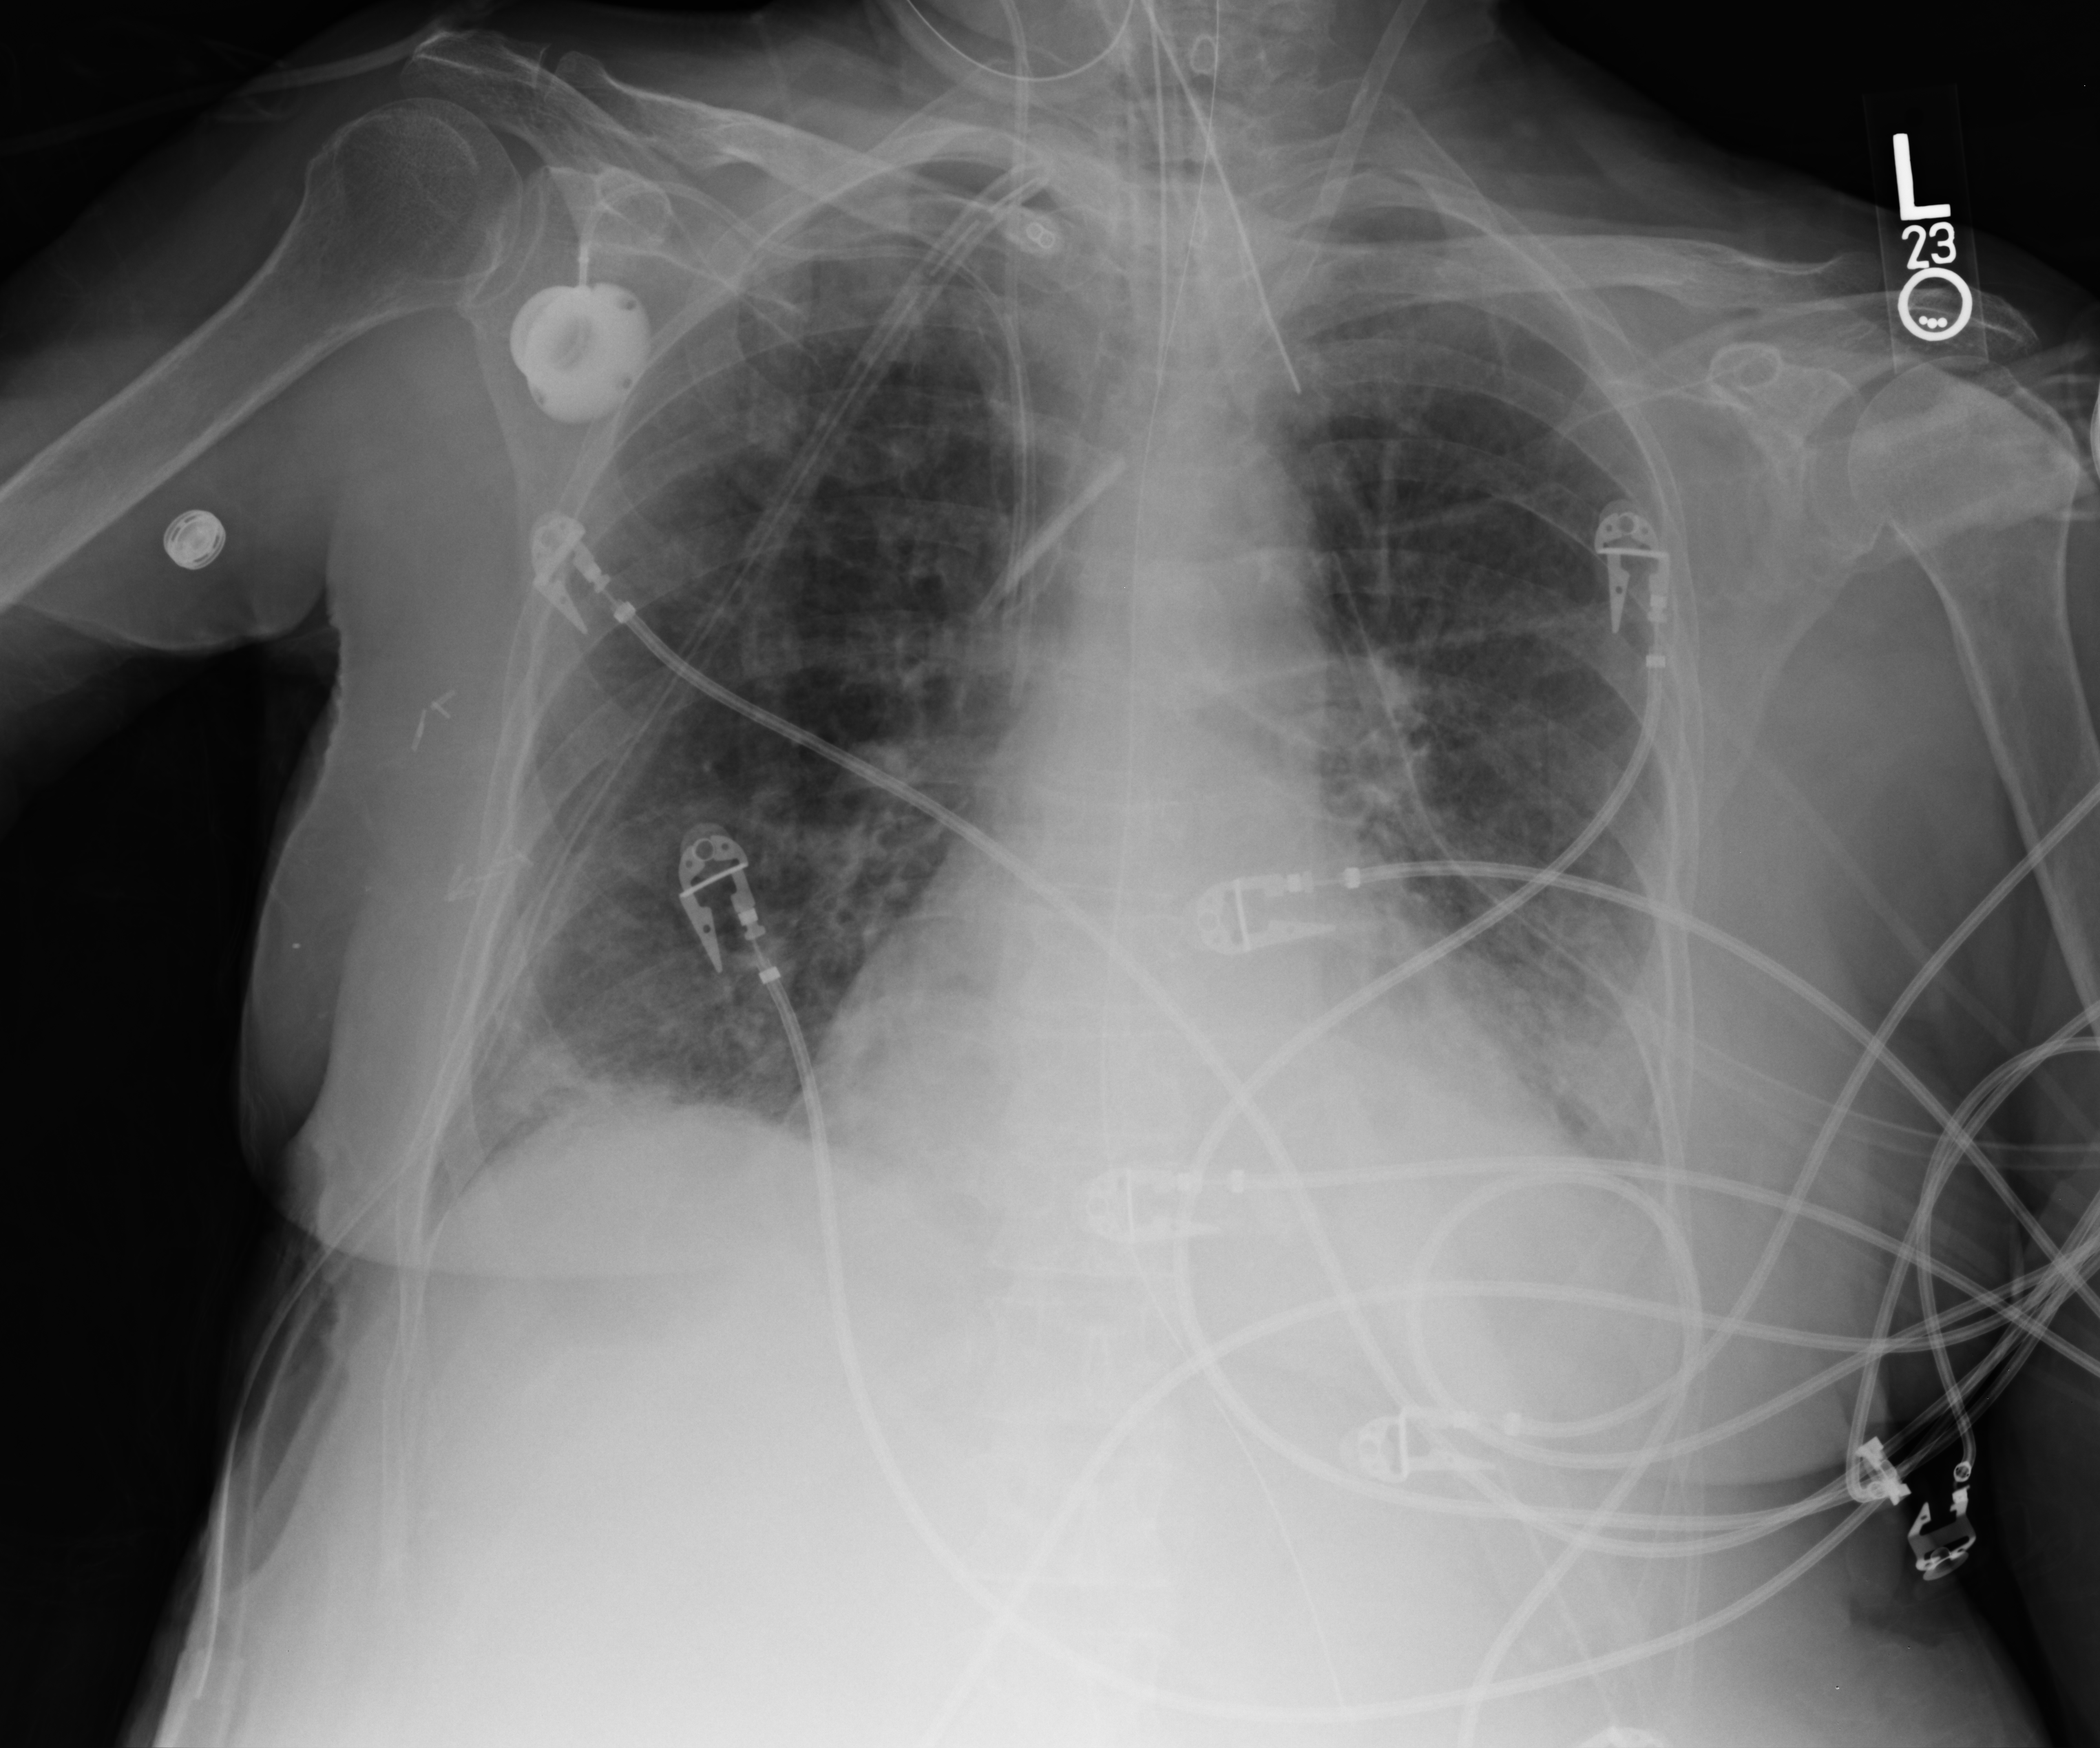
Chest X-ray (portable); anteroposterior (AP) projection. Patient hospitalised with COVID-19; female, aged 60–74 years.
Admission-level facts for this patient (not findings on this image; timing relative to this image not recorded):
- mechanically ventilated during this hospital stay: yes